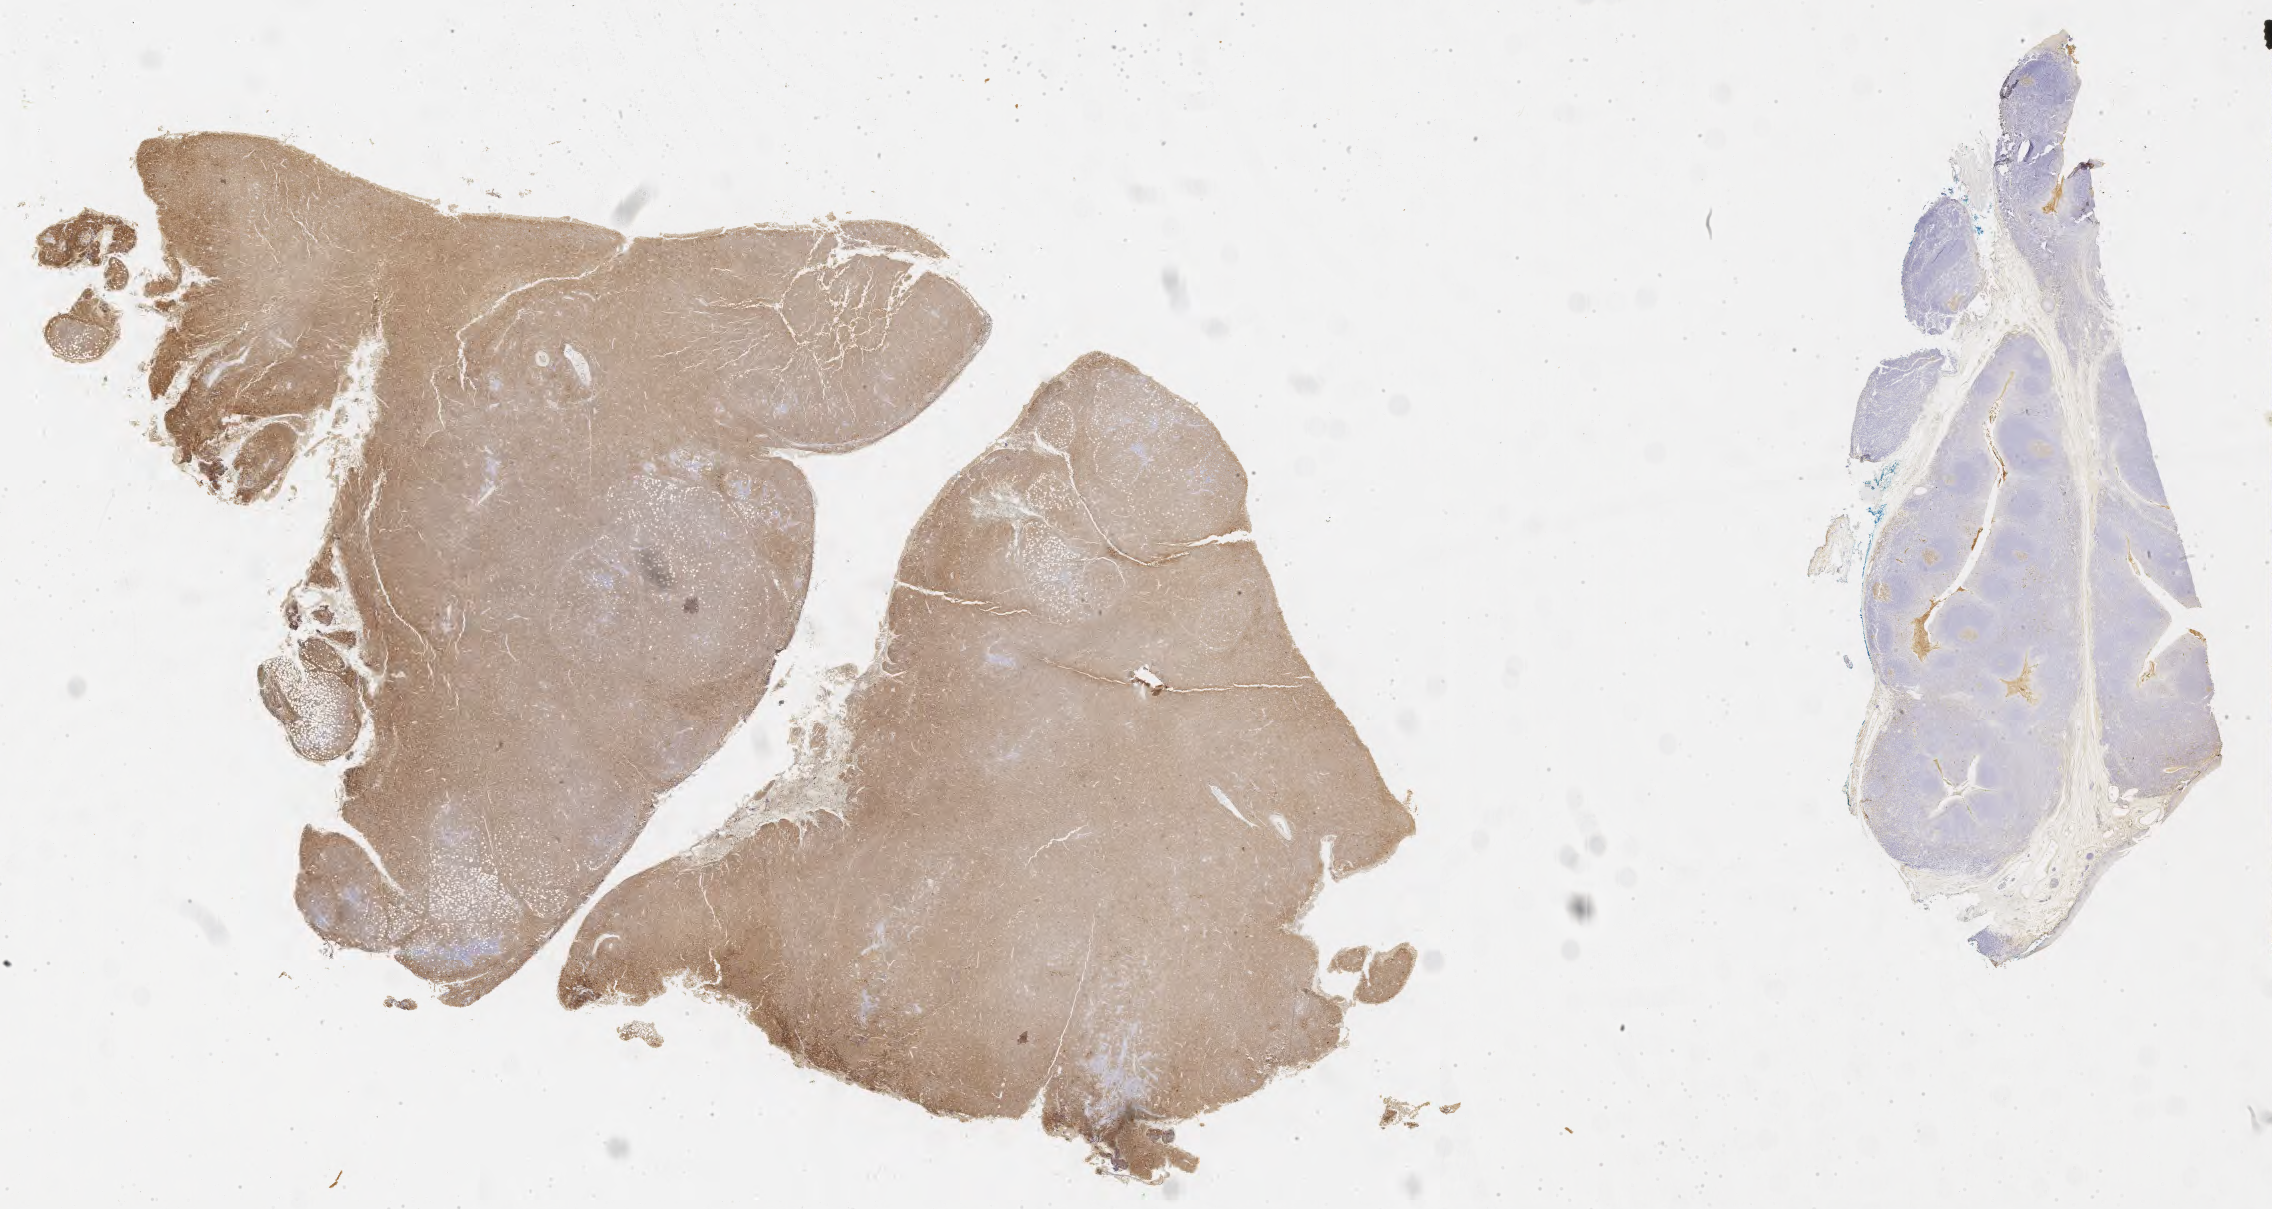
IHC for CD10, whole-slide image, low-resolution overview of the scanned area, about 36.7 x 19.5 mm, specimen: tumor tissue, anatomic site: peritoneum. Patient: male, age at initial diagnosis 9 years.
- histologic diagnosis: Burkitt lymphoma, NOS